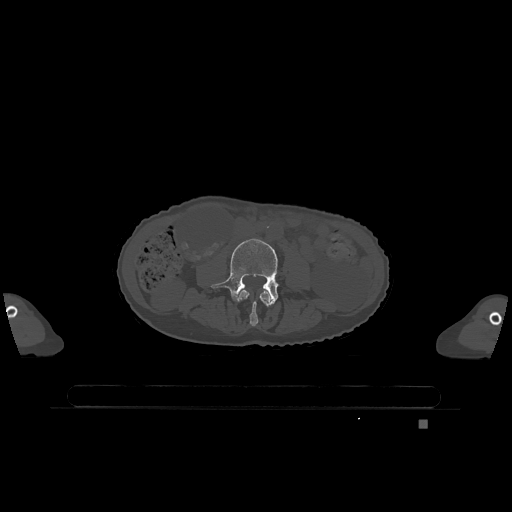
CT including the spine, one axial slice. Slice 316 of 1317 in the series (ordered by position). Bone window (W 1800 / L 400 HU). 512 × 512 image matrix, field of view 500 × 500 mm. Female patient, age 74 years. From the clinical record (not read from this slice): primary cancer: lung.
Outlined on this slice (semi-automatically segmented with operator editing):
- L3 vertebra: bounding box <239,289,271,326> (left, top, right, bottom; pixels)
- L4 vertebra: <210,239,278,305>